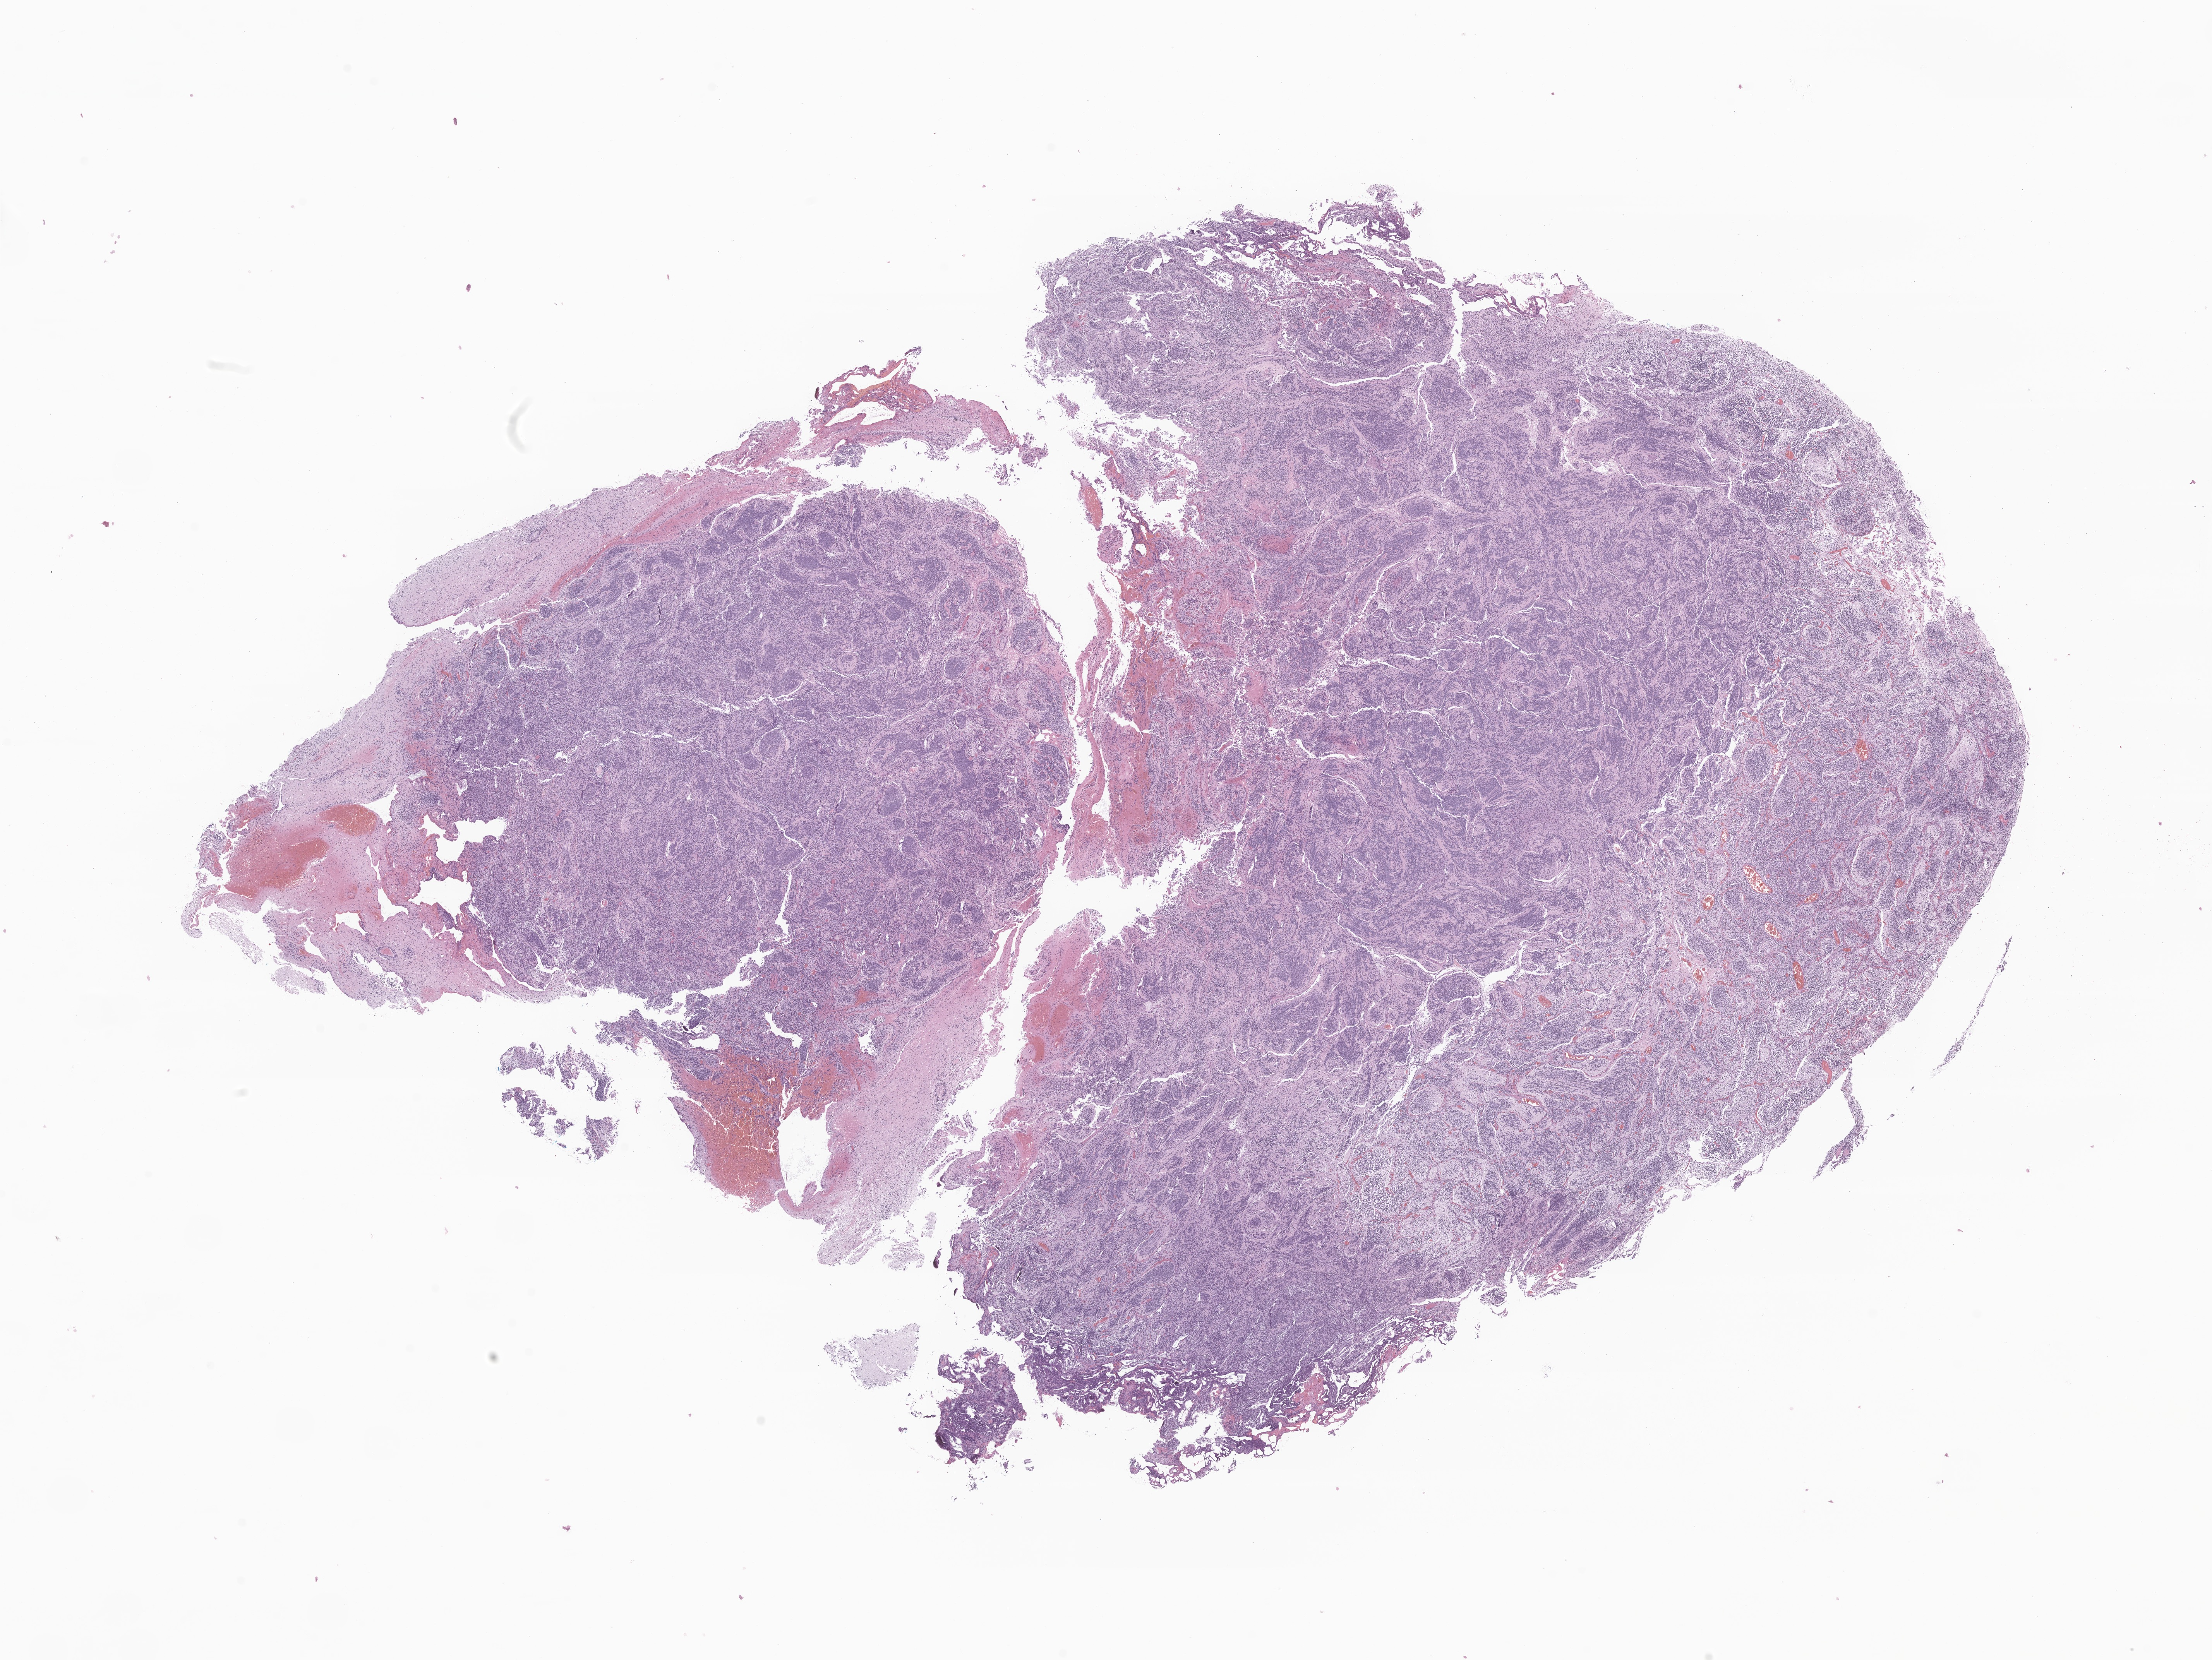
H&E whole-slide image of tumor tissue from the cerebellum, shown as a low-resolution overview of the whole scanned area (about 24.1 x 18.1 mm); formalin-fixed, paraffin-embedded (FFPE) tissue. Female patient, age 213 days.
Recorded diagnosis: Medulloblastoma, NOS.